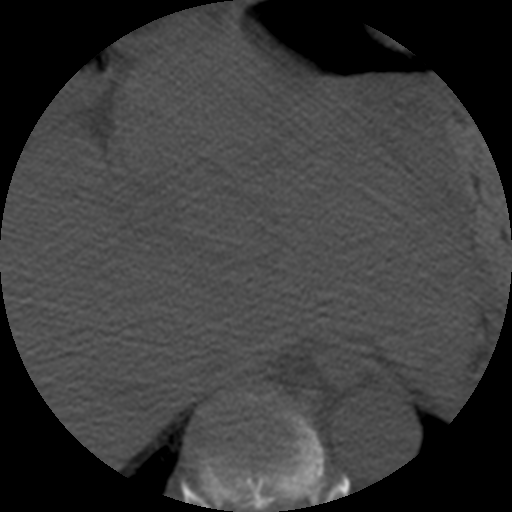
CT including the spine, one axial slice. Slice 279 of 508 in the series (ordered by position). Reconstruction kernel STANDARD. 120 kVp. Bone window (W 1800 / L 400 HU). 512 × 512 image matrix, field of view 160 × 160 mm. Patient age 57 years. From the clinical record (not read from this slice): primary cancer: prostate.
Structures marked on this image (semi-automatic segmentation, software-assisted and operator-edited):
- T9 vertebra: box from (x=198, y=391) to (x=326, y=512) px